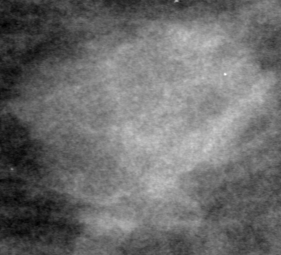
Cropped region of a digitized screen-film mammogram centred on a radiologist-marked abnormality, left breast, CC view, BI-RADS breast density category 3 (scale 1–4).
- Mass, shape lobulated, margins obscured; BI-RADS assessment category 0 (incomplete: needs additional imaging); subtlety rating 5 on a 1 (subtle) to 5 (obvious) scale; pathology result (as recorded, not read from the image): benign.